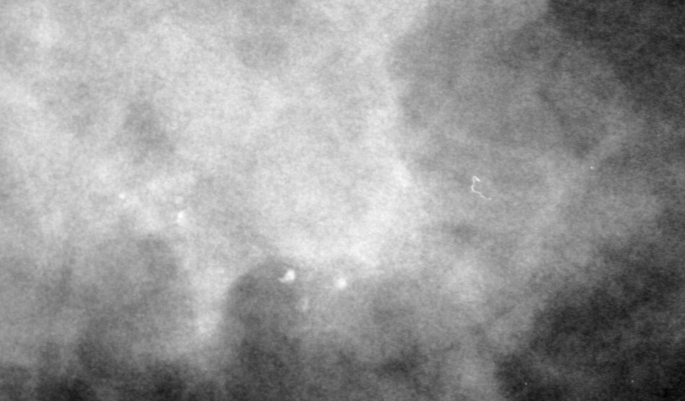
Crop from a digitized film mammogram around one marked abnormality; left breast; CC view; BI-RADS breast density category 3 (scale 1–4).
Finding: calcifications, morphology round and regular / pleomorphic, distribution clustered; BI-RADS assessment category 0 (incomplete: needs additional imaging); pathology result (as recorded, not read from the image): benign.